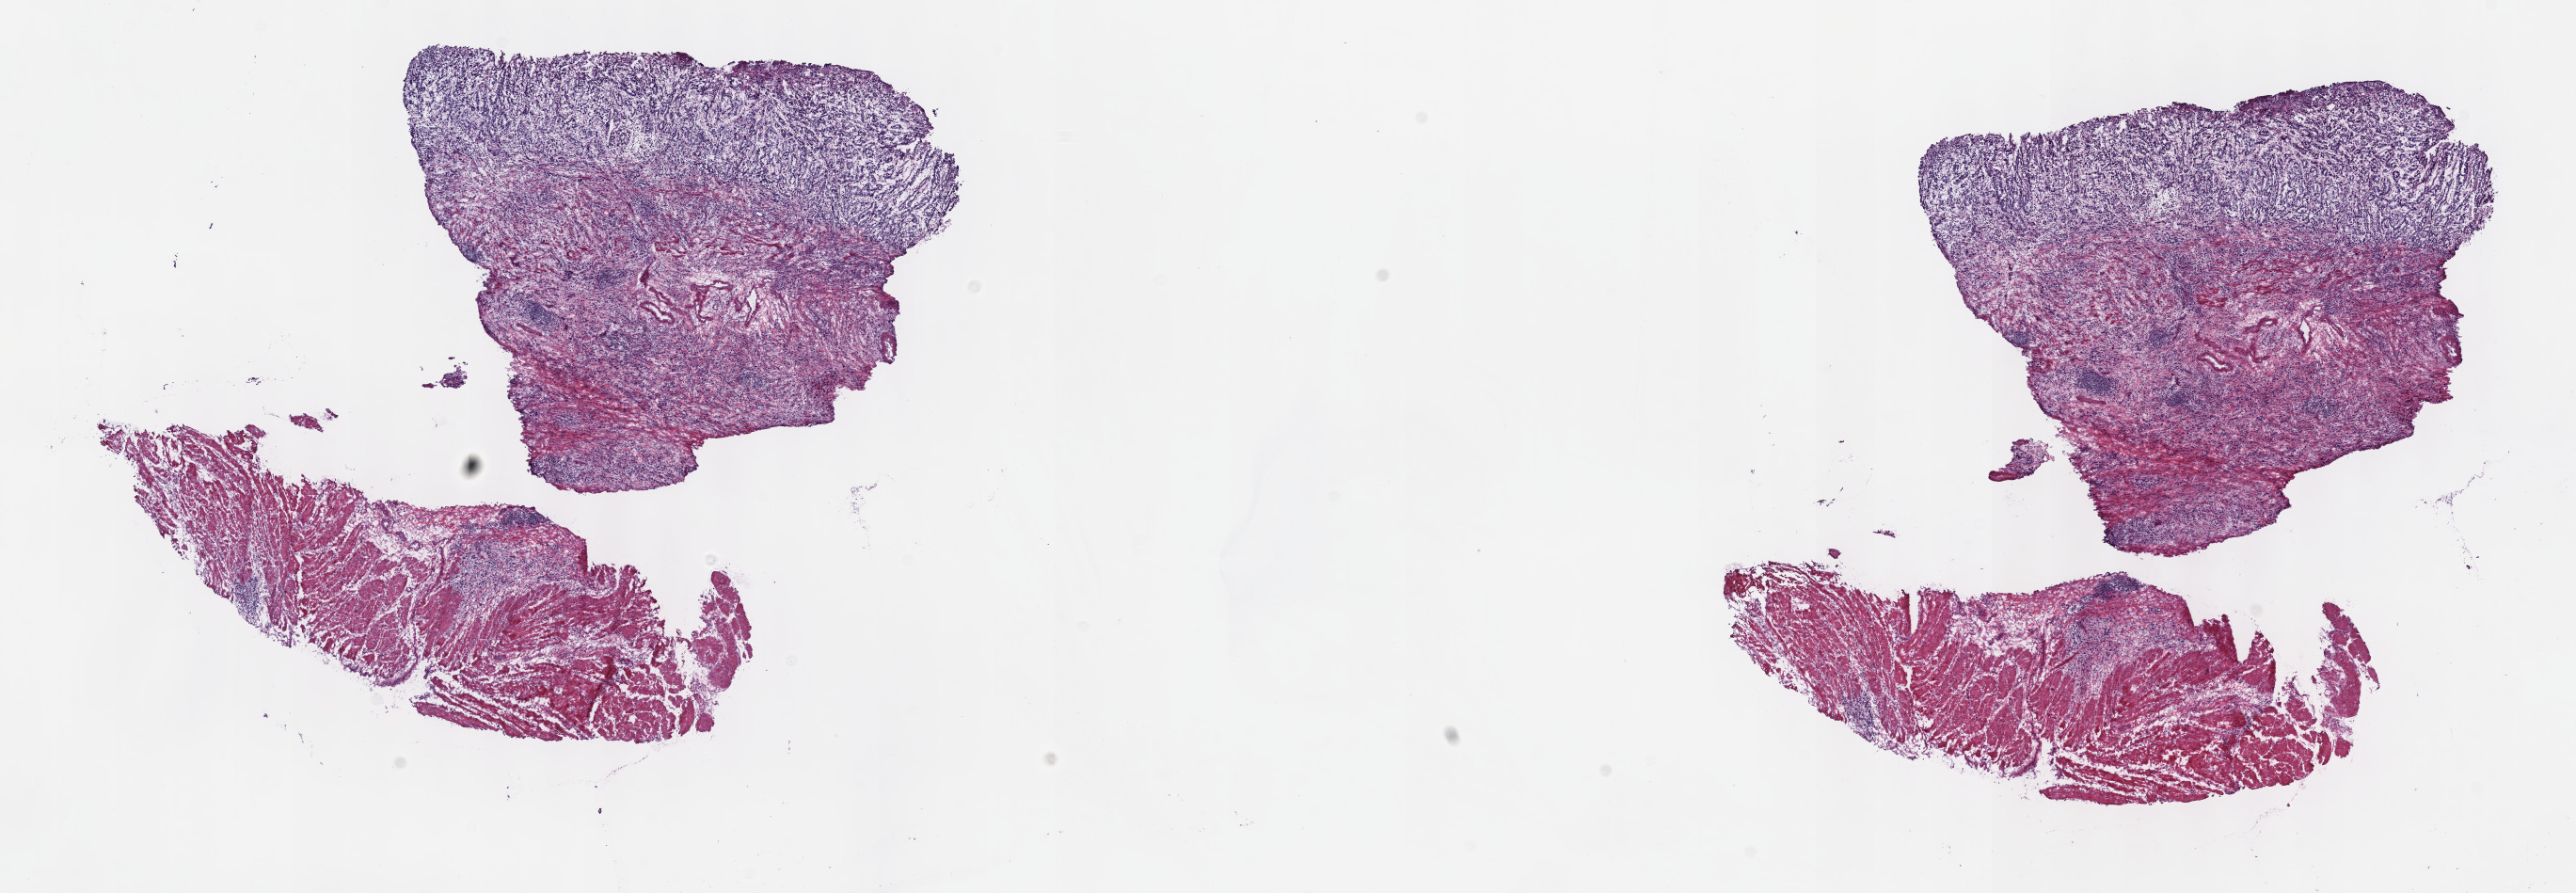
Digitized H&E tissue section (whole slide) — low-resolution overview of the scanned area, about 22.1 x 7.7 mm; frozen section from the top of the tissue portion; sample: primary tumour, esophagus. Patient: male, age at initial diagnosis 51 years. Histologic grade: G3 (poorly differentiated). Pathologist review of this section (percent, as recorded): tumour cells 70%, tumour nuclei 70%, normal cells 0%, stromal cells 20%, necrosis 10%. Inflammatory infiltration, as recorded: lymphocyte infiltration 40%, monocyte infiltration 20%, neutrophil infiltration 20%.
Diagnosis: Adenocarcinoma, NOS (lower third of esophagus). Lymph nodes positive (case pathology): 14 of 39 examined. AJCC pathologic stage: IIIC (7th edition).